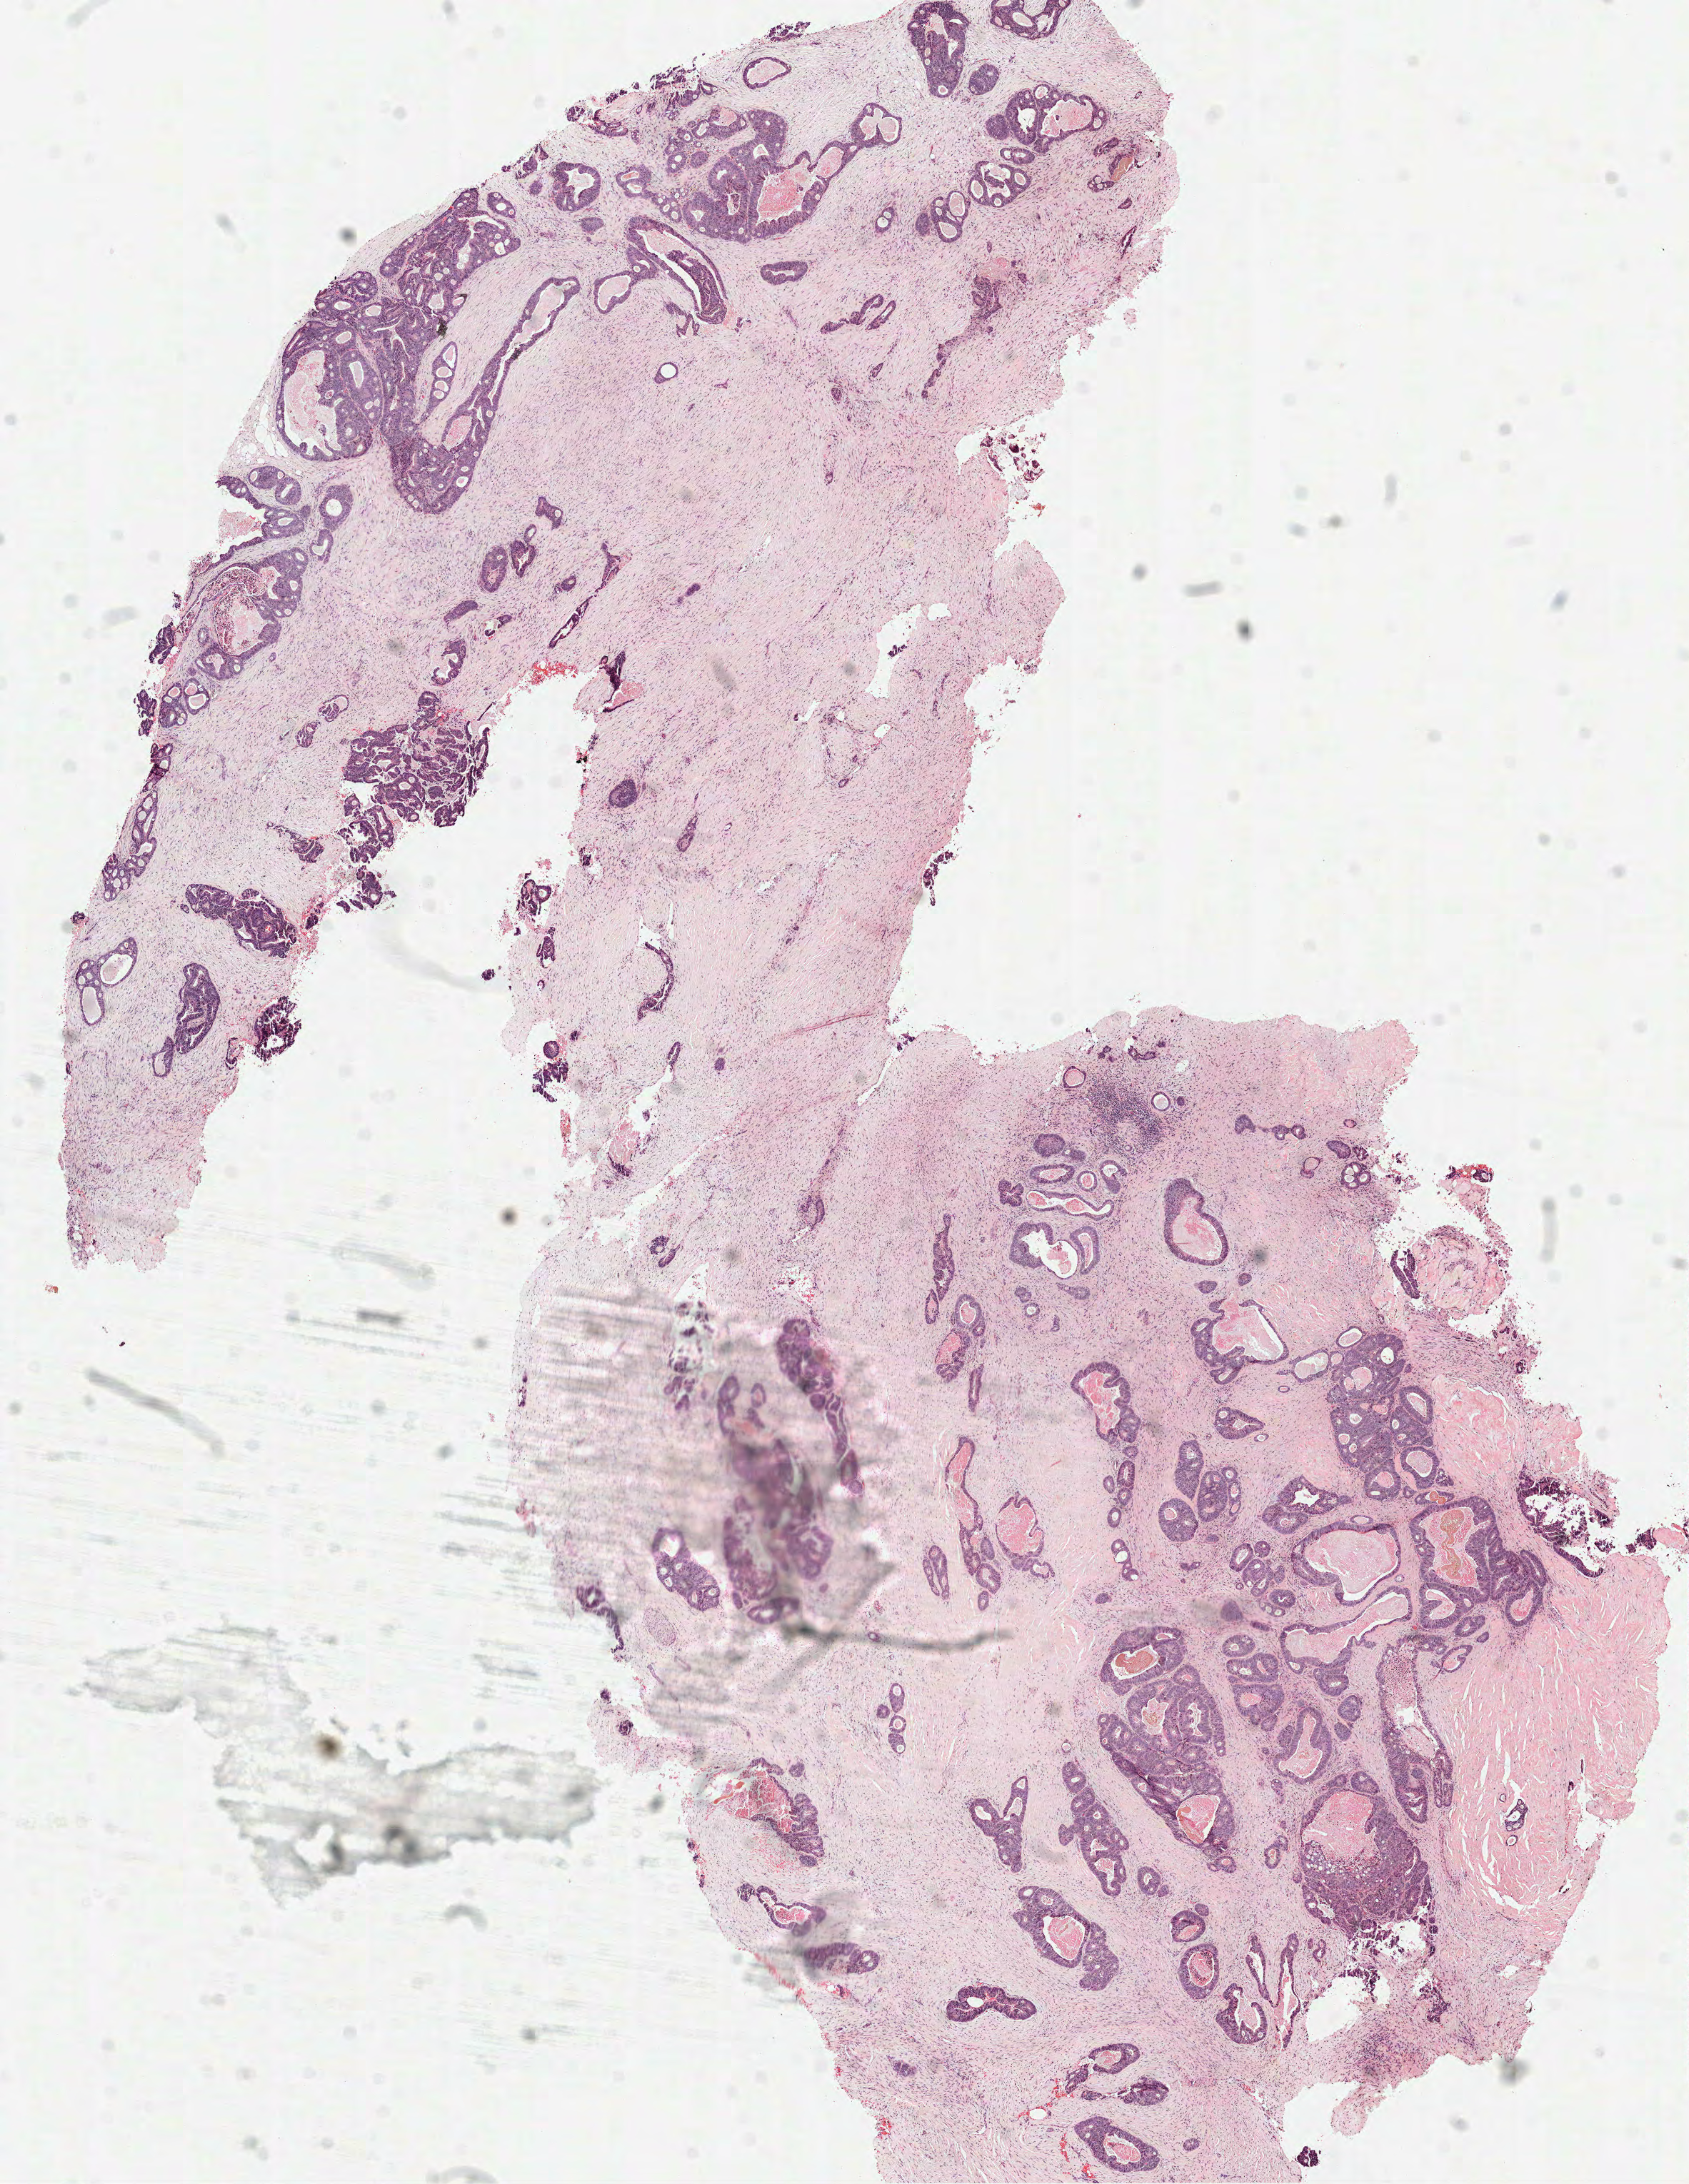
Digitized Hematoxylin and eosin (H&E) stained tissue section (whole slide) — low-resolution overview of the scanned area, about 9.5 x 12.3 mm (slide scanned at 40x), frozen section from the top of the tissue portion, primary tumour sample from the rectum. Male patient; age at initial diagnosis 56 years. Slide review estimates, as recorded: tumour cells 60%, tumour nuclei 80%, normal cells 0%, stromal cells 30%, necrosis 10%.
Diagnosis: Adenocarcinoma, NOS (rectosigmoid junction).